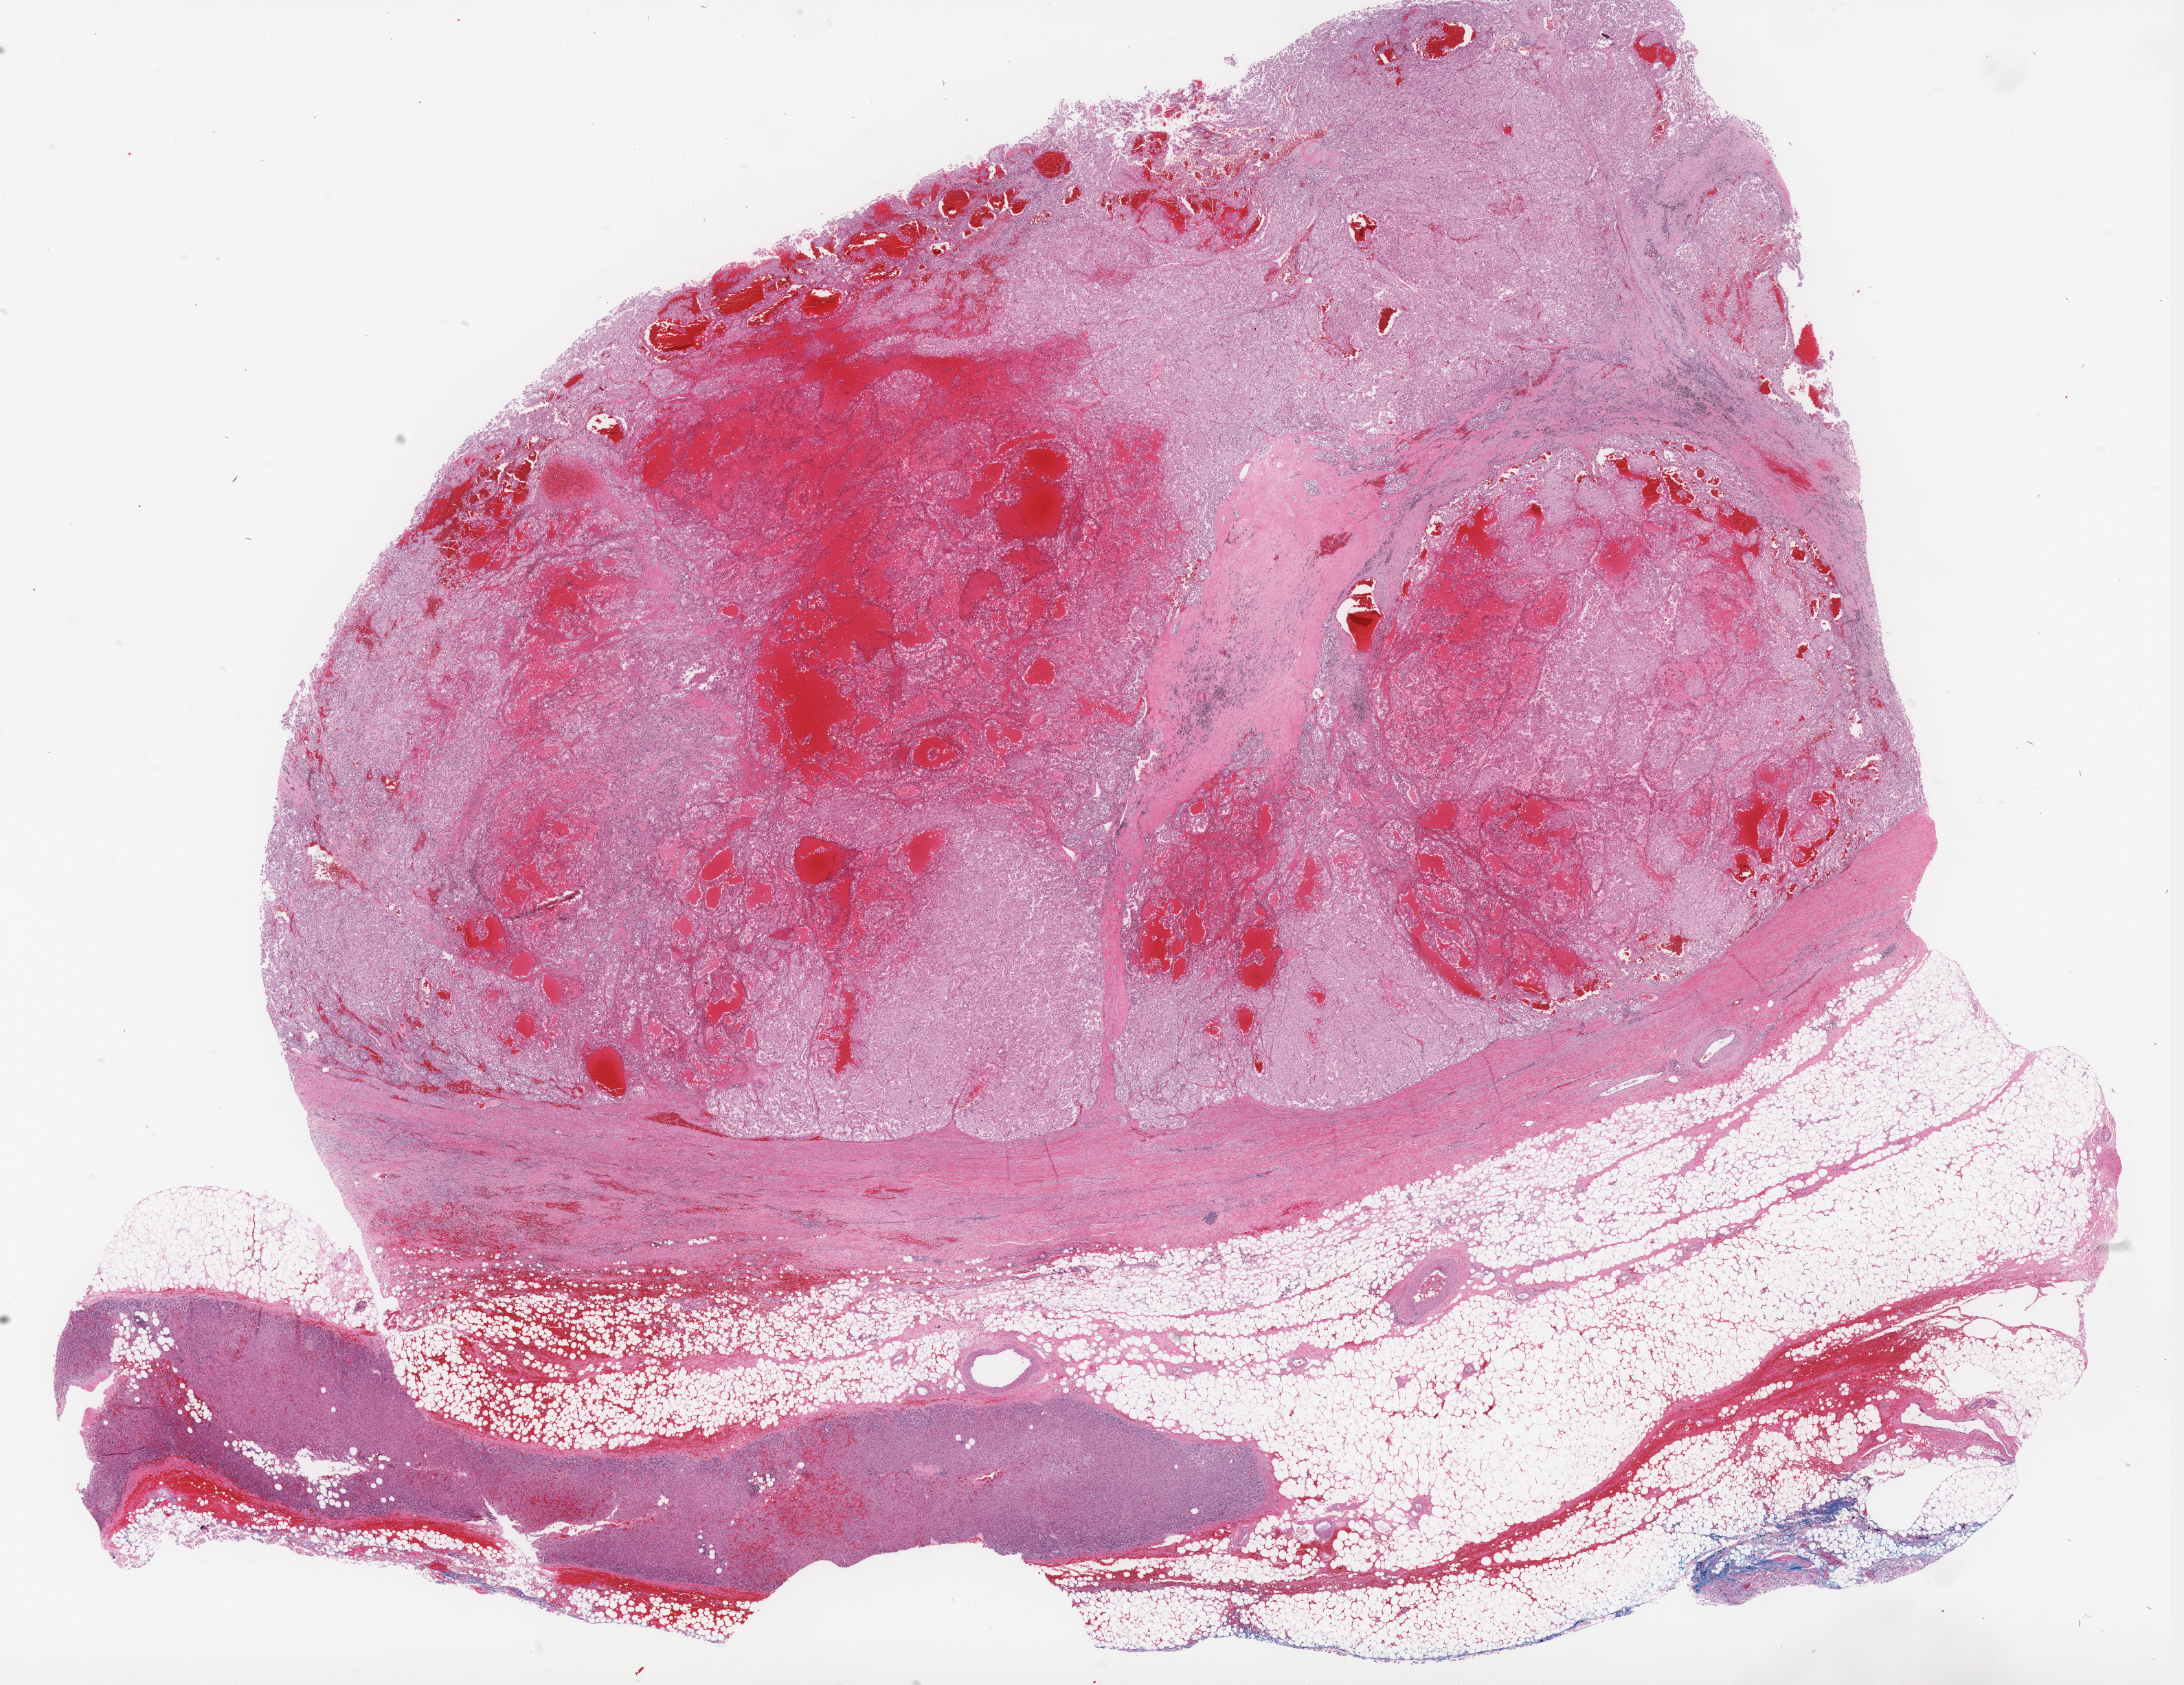
H&E whole-slide image, low-resolution overview of the scanned area, about 25.4 x 19.6 mm, formalin-fixed paraffin-embedded (FFPE) diagnostic section, kidney, primary tumour sample. Female patient; age at initial diagnosis 56 years.
Histologic diagnosis: Renal cell carcinoma, chromophobe type. Laterality: left. TNM: T2 NX M0. AJCC pathologic stage: II (5th edition).